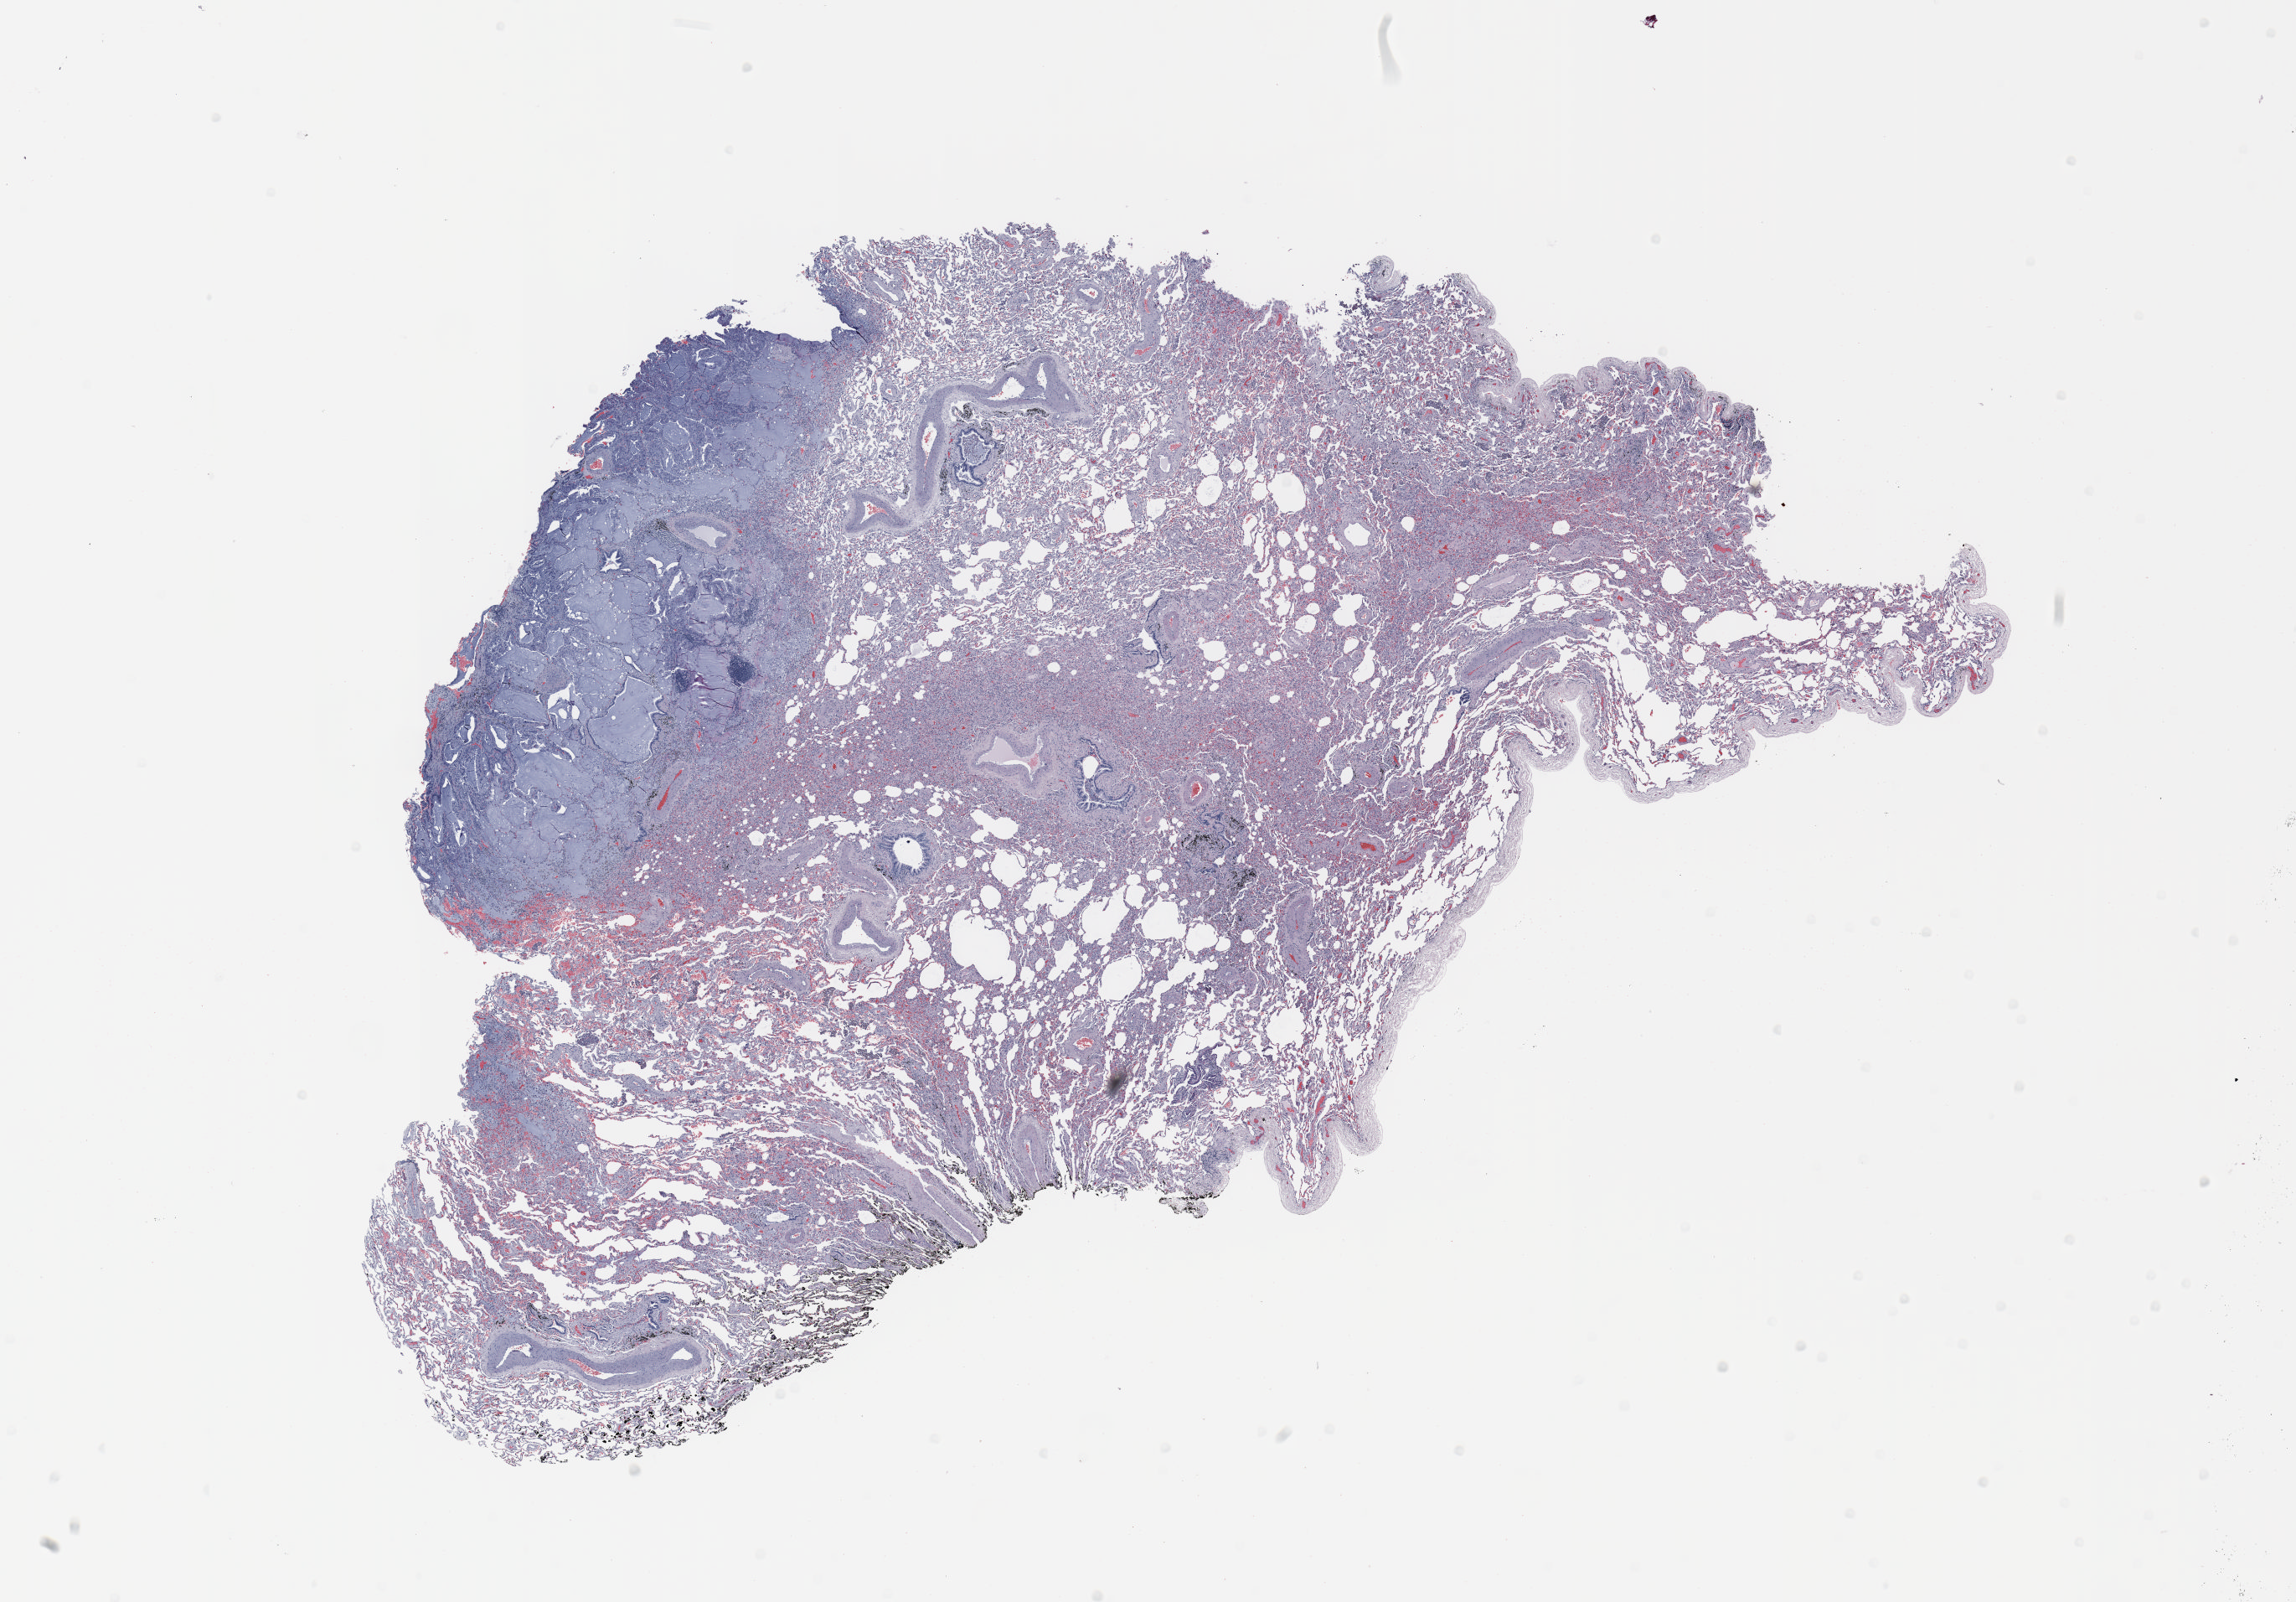
H&E whole-slide image — whole scanned area (about 22.0 x 15.4 mm) shown as a low-resolution overview; formalin-fixed paraffin-embedded (FFPE) section; lung. Male, age 65 at enrolment. Grade: well differentiated (G1).
Stage (AJCC 6th edition): IB. Tumour size (pathology): 10 mm. Participant's lung-cancer diagnosis: Adenocarcinoma, NOS. ICD-O-3 topography: lower lobe of lung (C34.3). Primary tumour location (clinical record): left lower lobe.